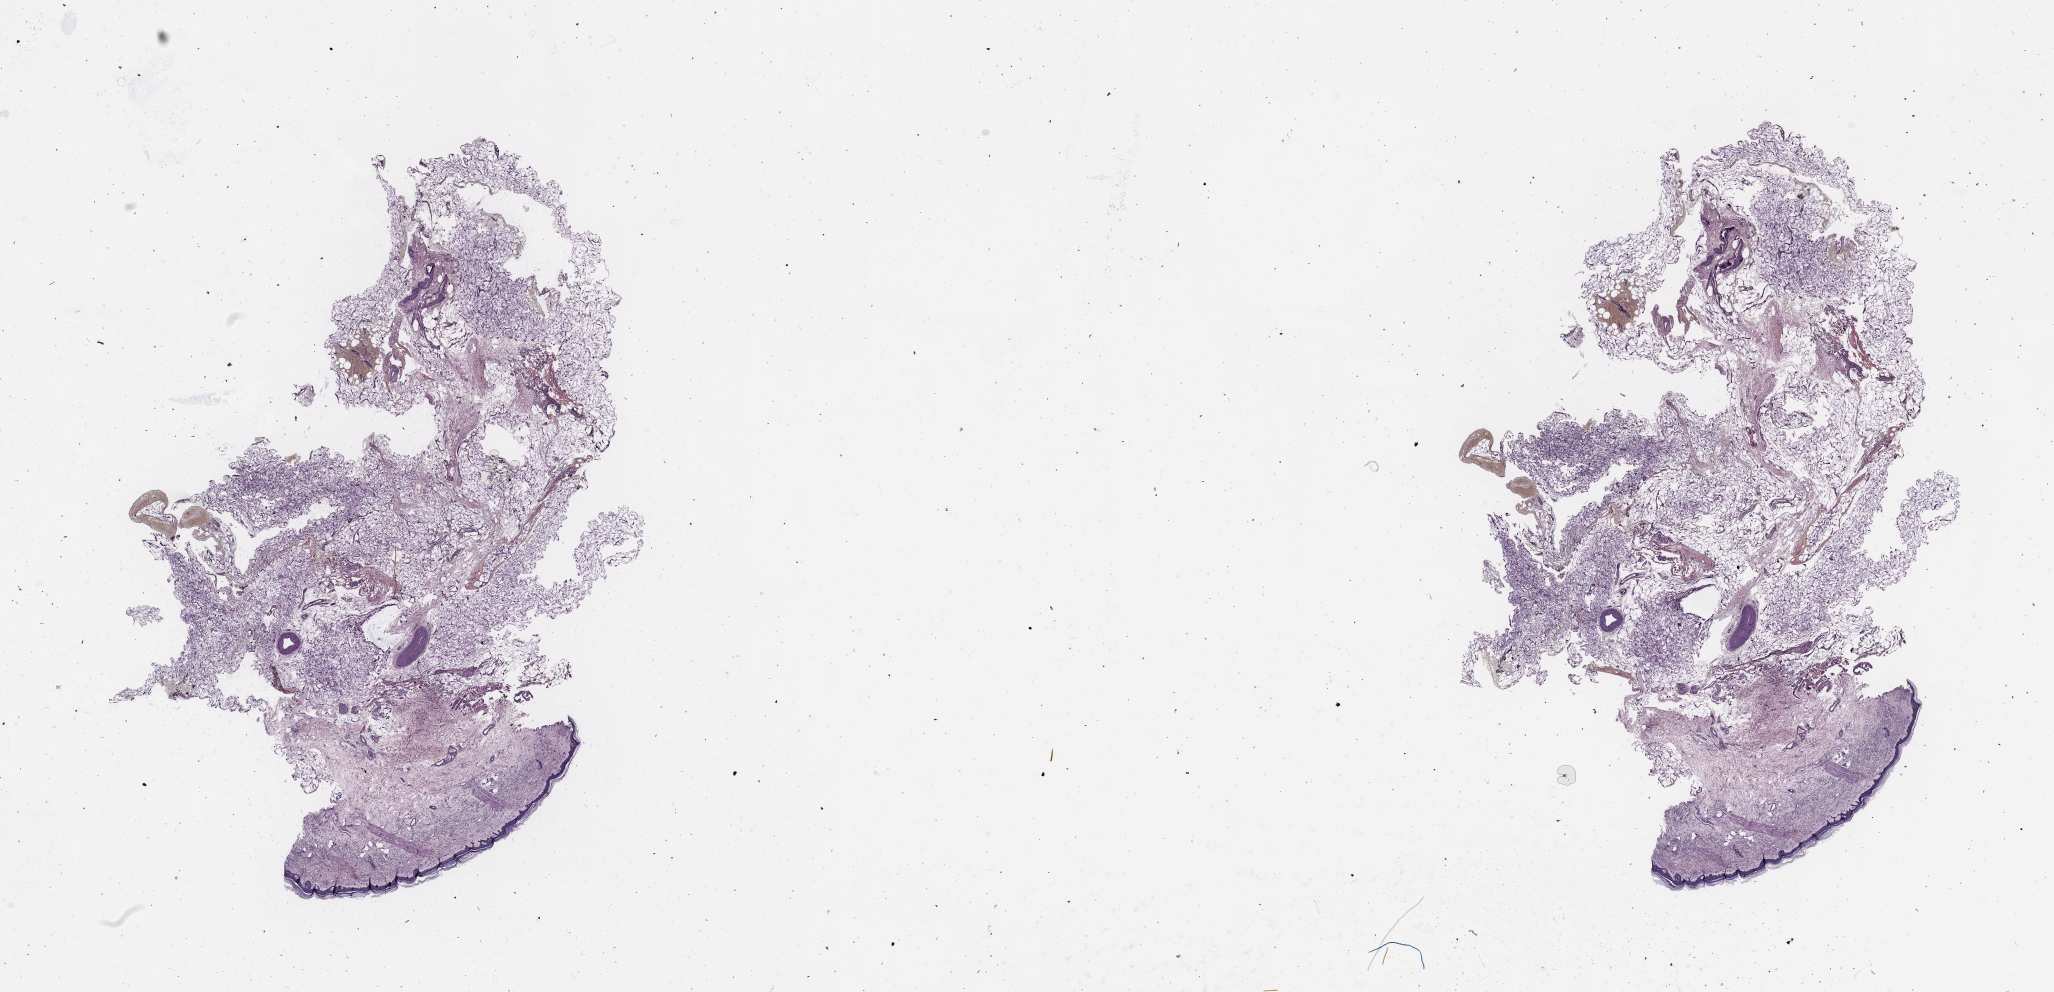
Digitized H&E-stained tissue section (whole slide), low-resolution overview of the scanned area, about 32.5 x 15.7 mm. Normal (non-tumour) tissue sample, sampled site: skin. 78-year-old female patient.
This section: normal (non-tumour) tissue from the same patient. Patient diagnosis: Malignant melanoma, NOS.